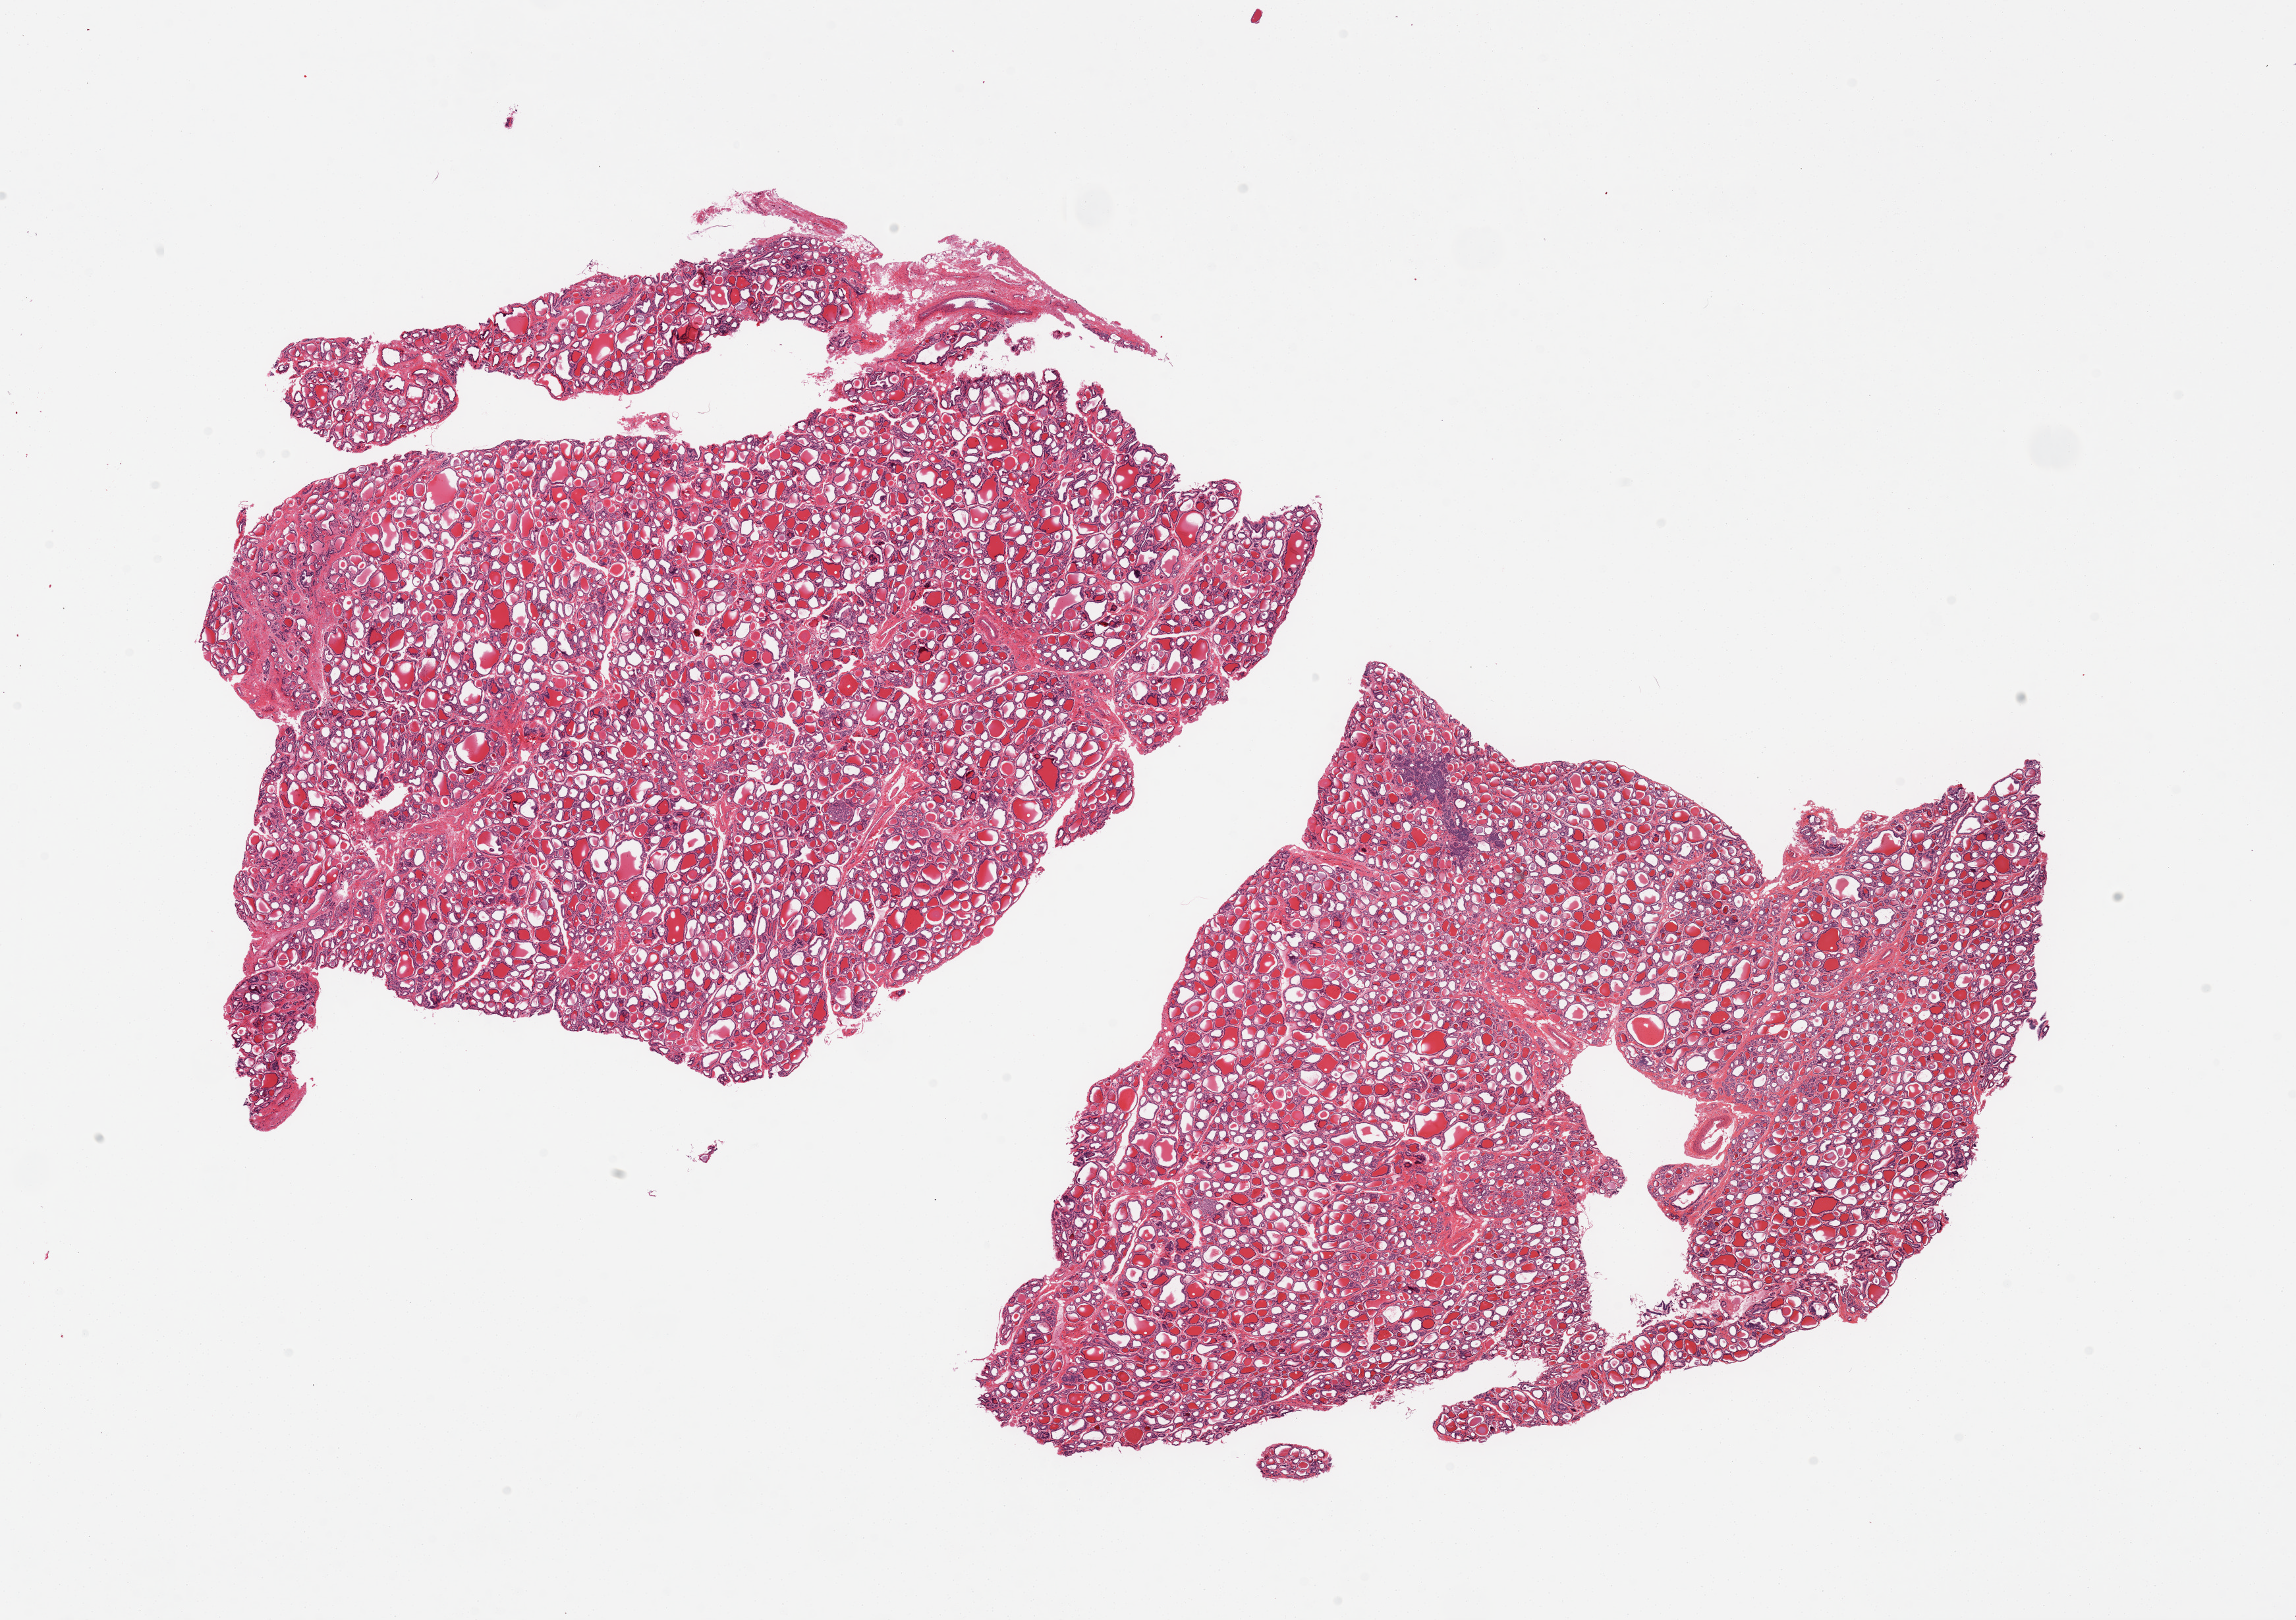
Whole-slide image, hematoxylin and eosin (H&E) stain — shown as a low-resolution overview of the whole scanned area (about 27.6 x 19.4 mm, slide scanned at 20x), PAXgene-fixed, paraffin-embedded tissue, section of thyroid (target tissue), tissue donor sample. Donor sex: male.
- reviewer comment on this tissue sample: 2 pieces, focus of solid cell nests